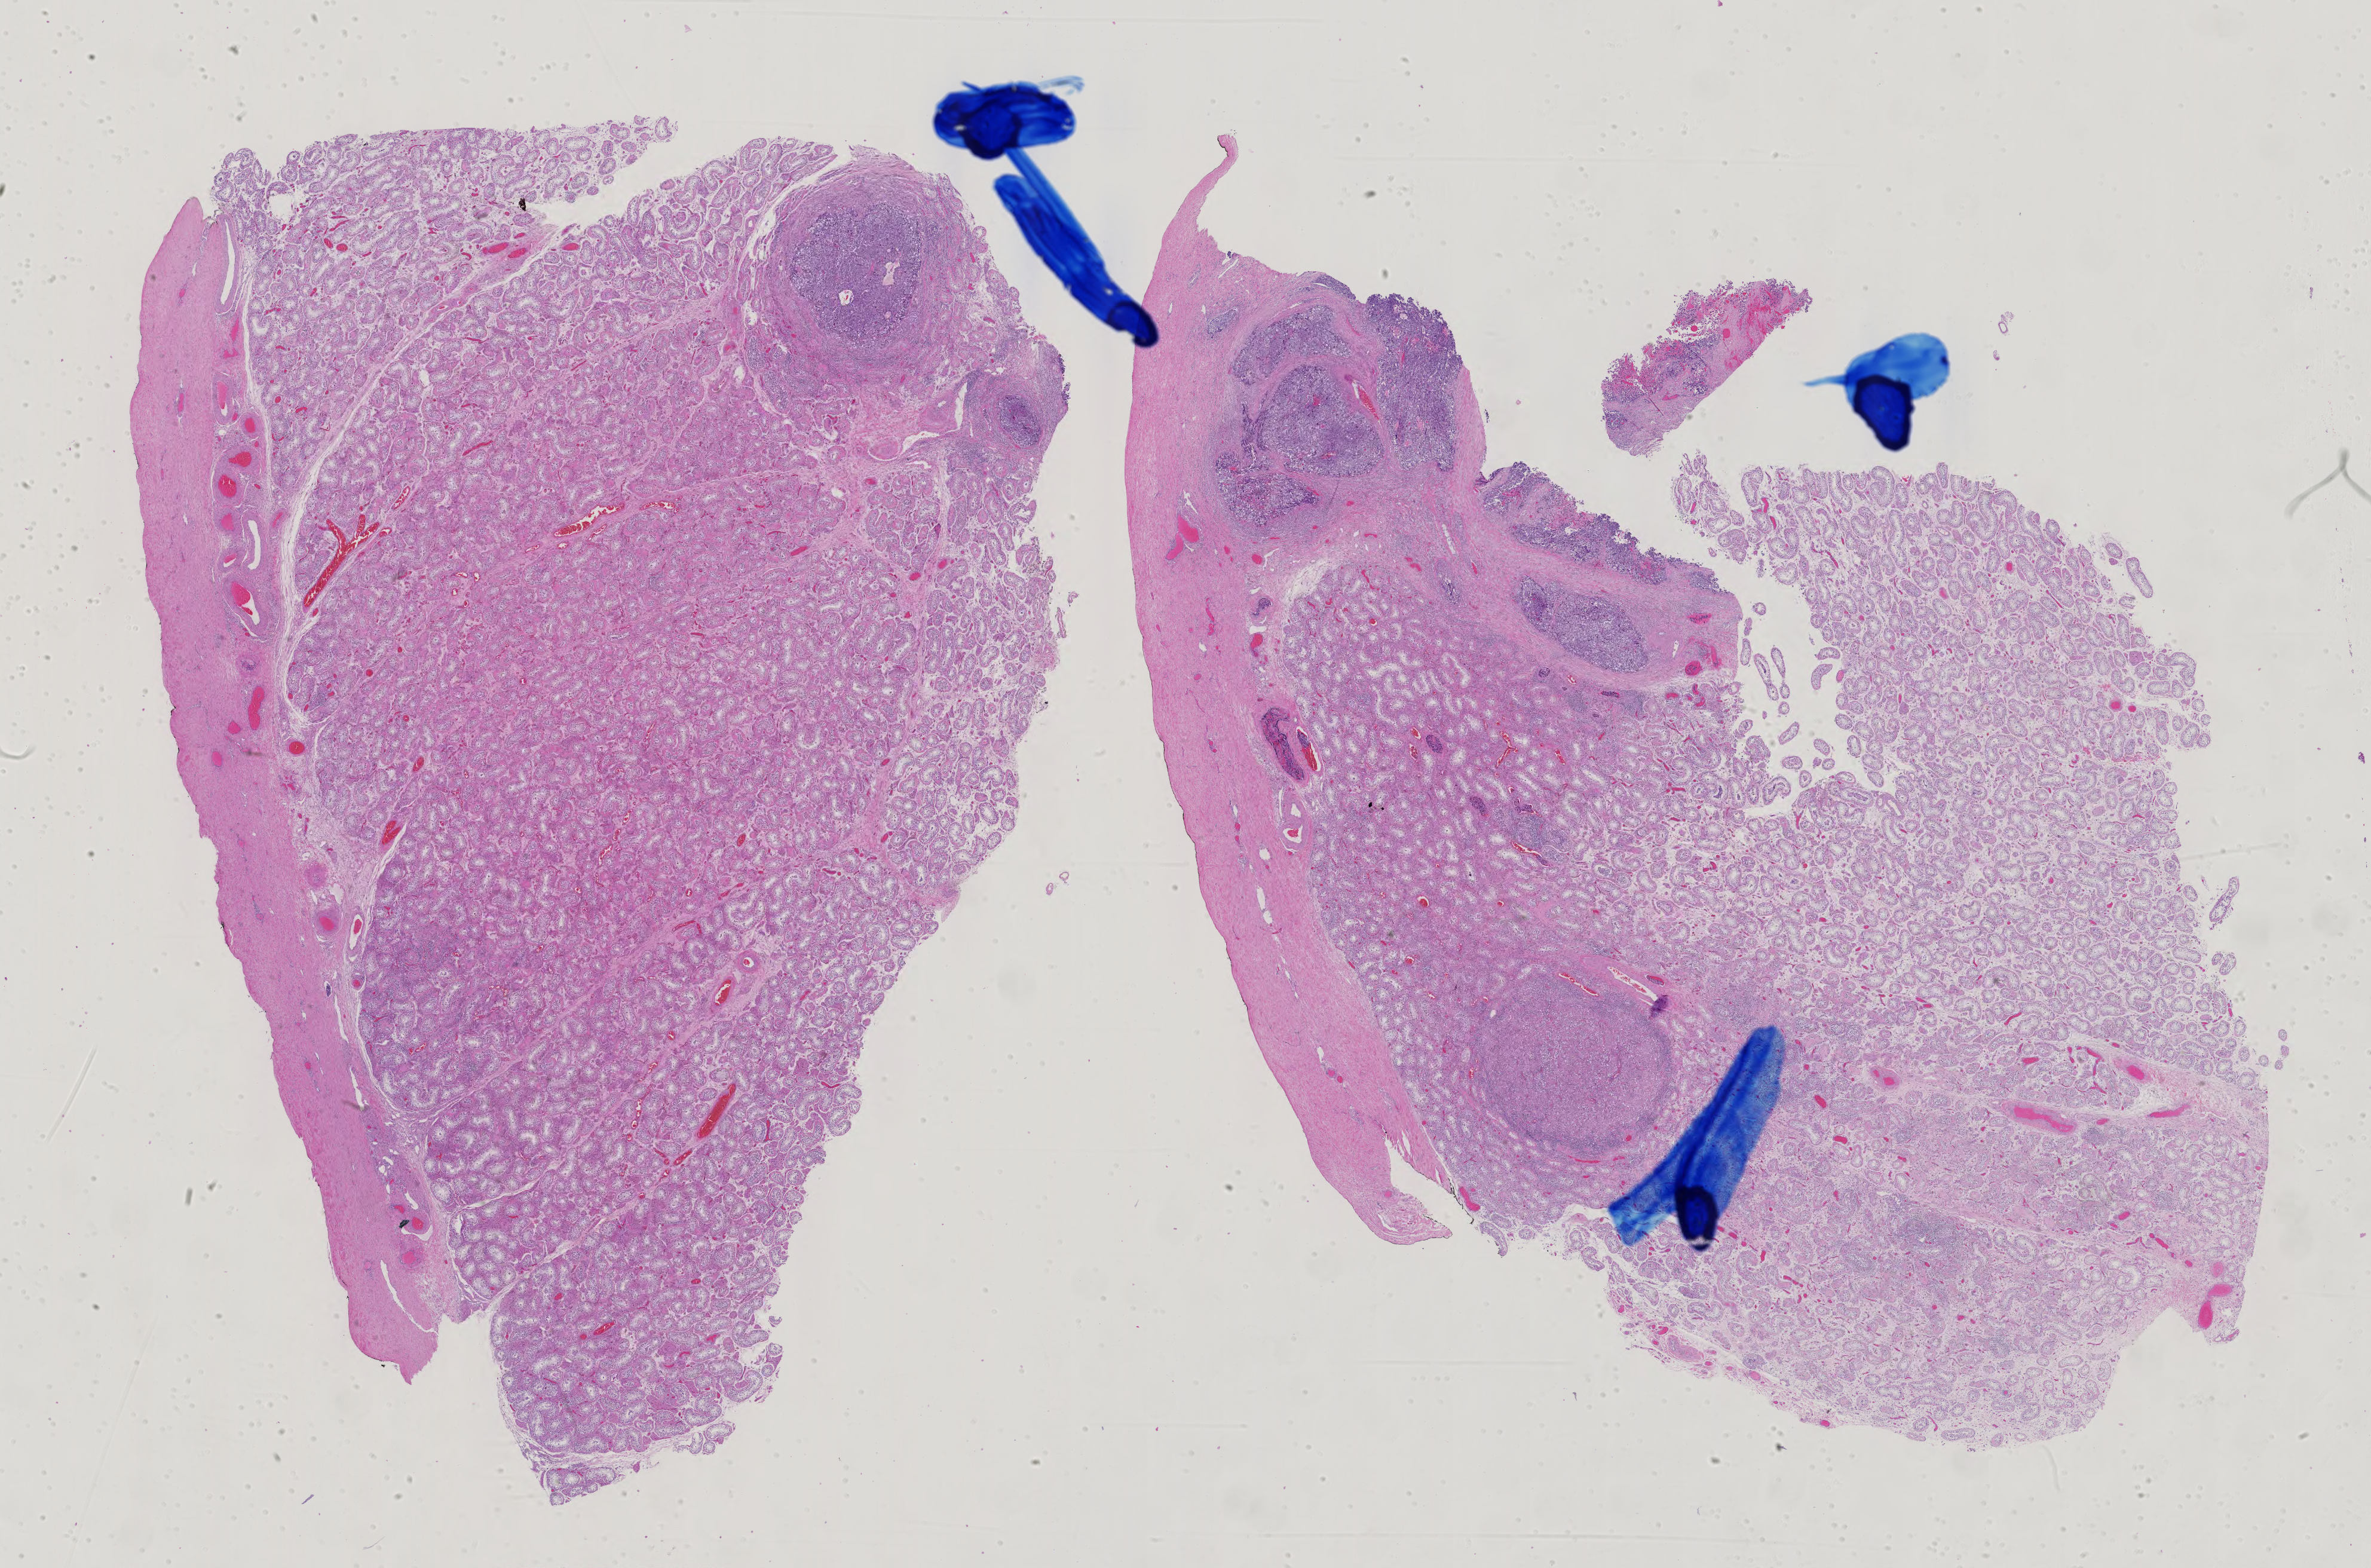
Hematoxylin and eosin (H&E) stained whole-slide image — shown as a low-resolution overview of the whole scanned area (about 28.9 x 19.1 mm, slide scanned at 40x); FFPE section; primary tumour sample from the testis. Male, age 33 years at initial diagnosis.
AJCC pathologic stage: IIA (7th edition). Pathologic diagnosis: Embryonal carcinoma, NOS.